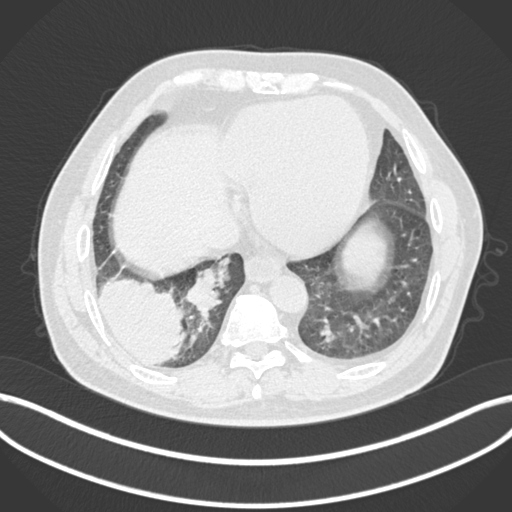
Chest CT, one axial slice. Position 37 of 200 along the scan axis. Reconstruction kernel B30f. Lung window (W 1500 / L -600 HU). 1 mm slice thickness. 512 × 512 image matrix, field of view 400 × 400 mm. Male patient, age 59 years.
Outlined on this slice (rectangle marked by the reading radiologist):
- lung tumour (recorded histology: adenocarcinoma): bounding box (x1, y1, x2, y2) in pixels: (96, 275, 188, 370)